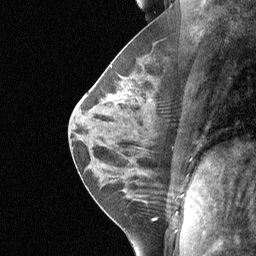
Breast MRI (dynamic contrast-enhanced), one sagittal slice. Position 29 of 64 along the scan axis. Dynamic contrast-enhanced study with each time point stored as its own series, time point 2 of 3 at this slice position (early post-contrast, ordered by acquisition time). 1.5 T. TE 4.8 ms, TR 27 ms. 2 mm slice thickness. 256 × 256 image matrix, field of view 200 × 200 mm. Patient: female, 27 years. Case-level facts recorded for this patient, not image findings: setting: breast cancer imaged before/during neoadjuvant chemotherapy; receptor status: HR-positive, HER2-negative.
Annotated regions visible in this slice (semi-automatically segmented with operator editing):
- analysis volume of interest (the breast-tissue region the enhancement analysis was run in; not a lesion): box from (x=89, y=45) to (x=157, y=149) px
- tumour enhancement mask (voxels above the 90 % enhancement threshold inside the analysis volume of interest): (x=116, y=97)–(x=119, y=99)